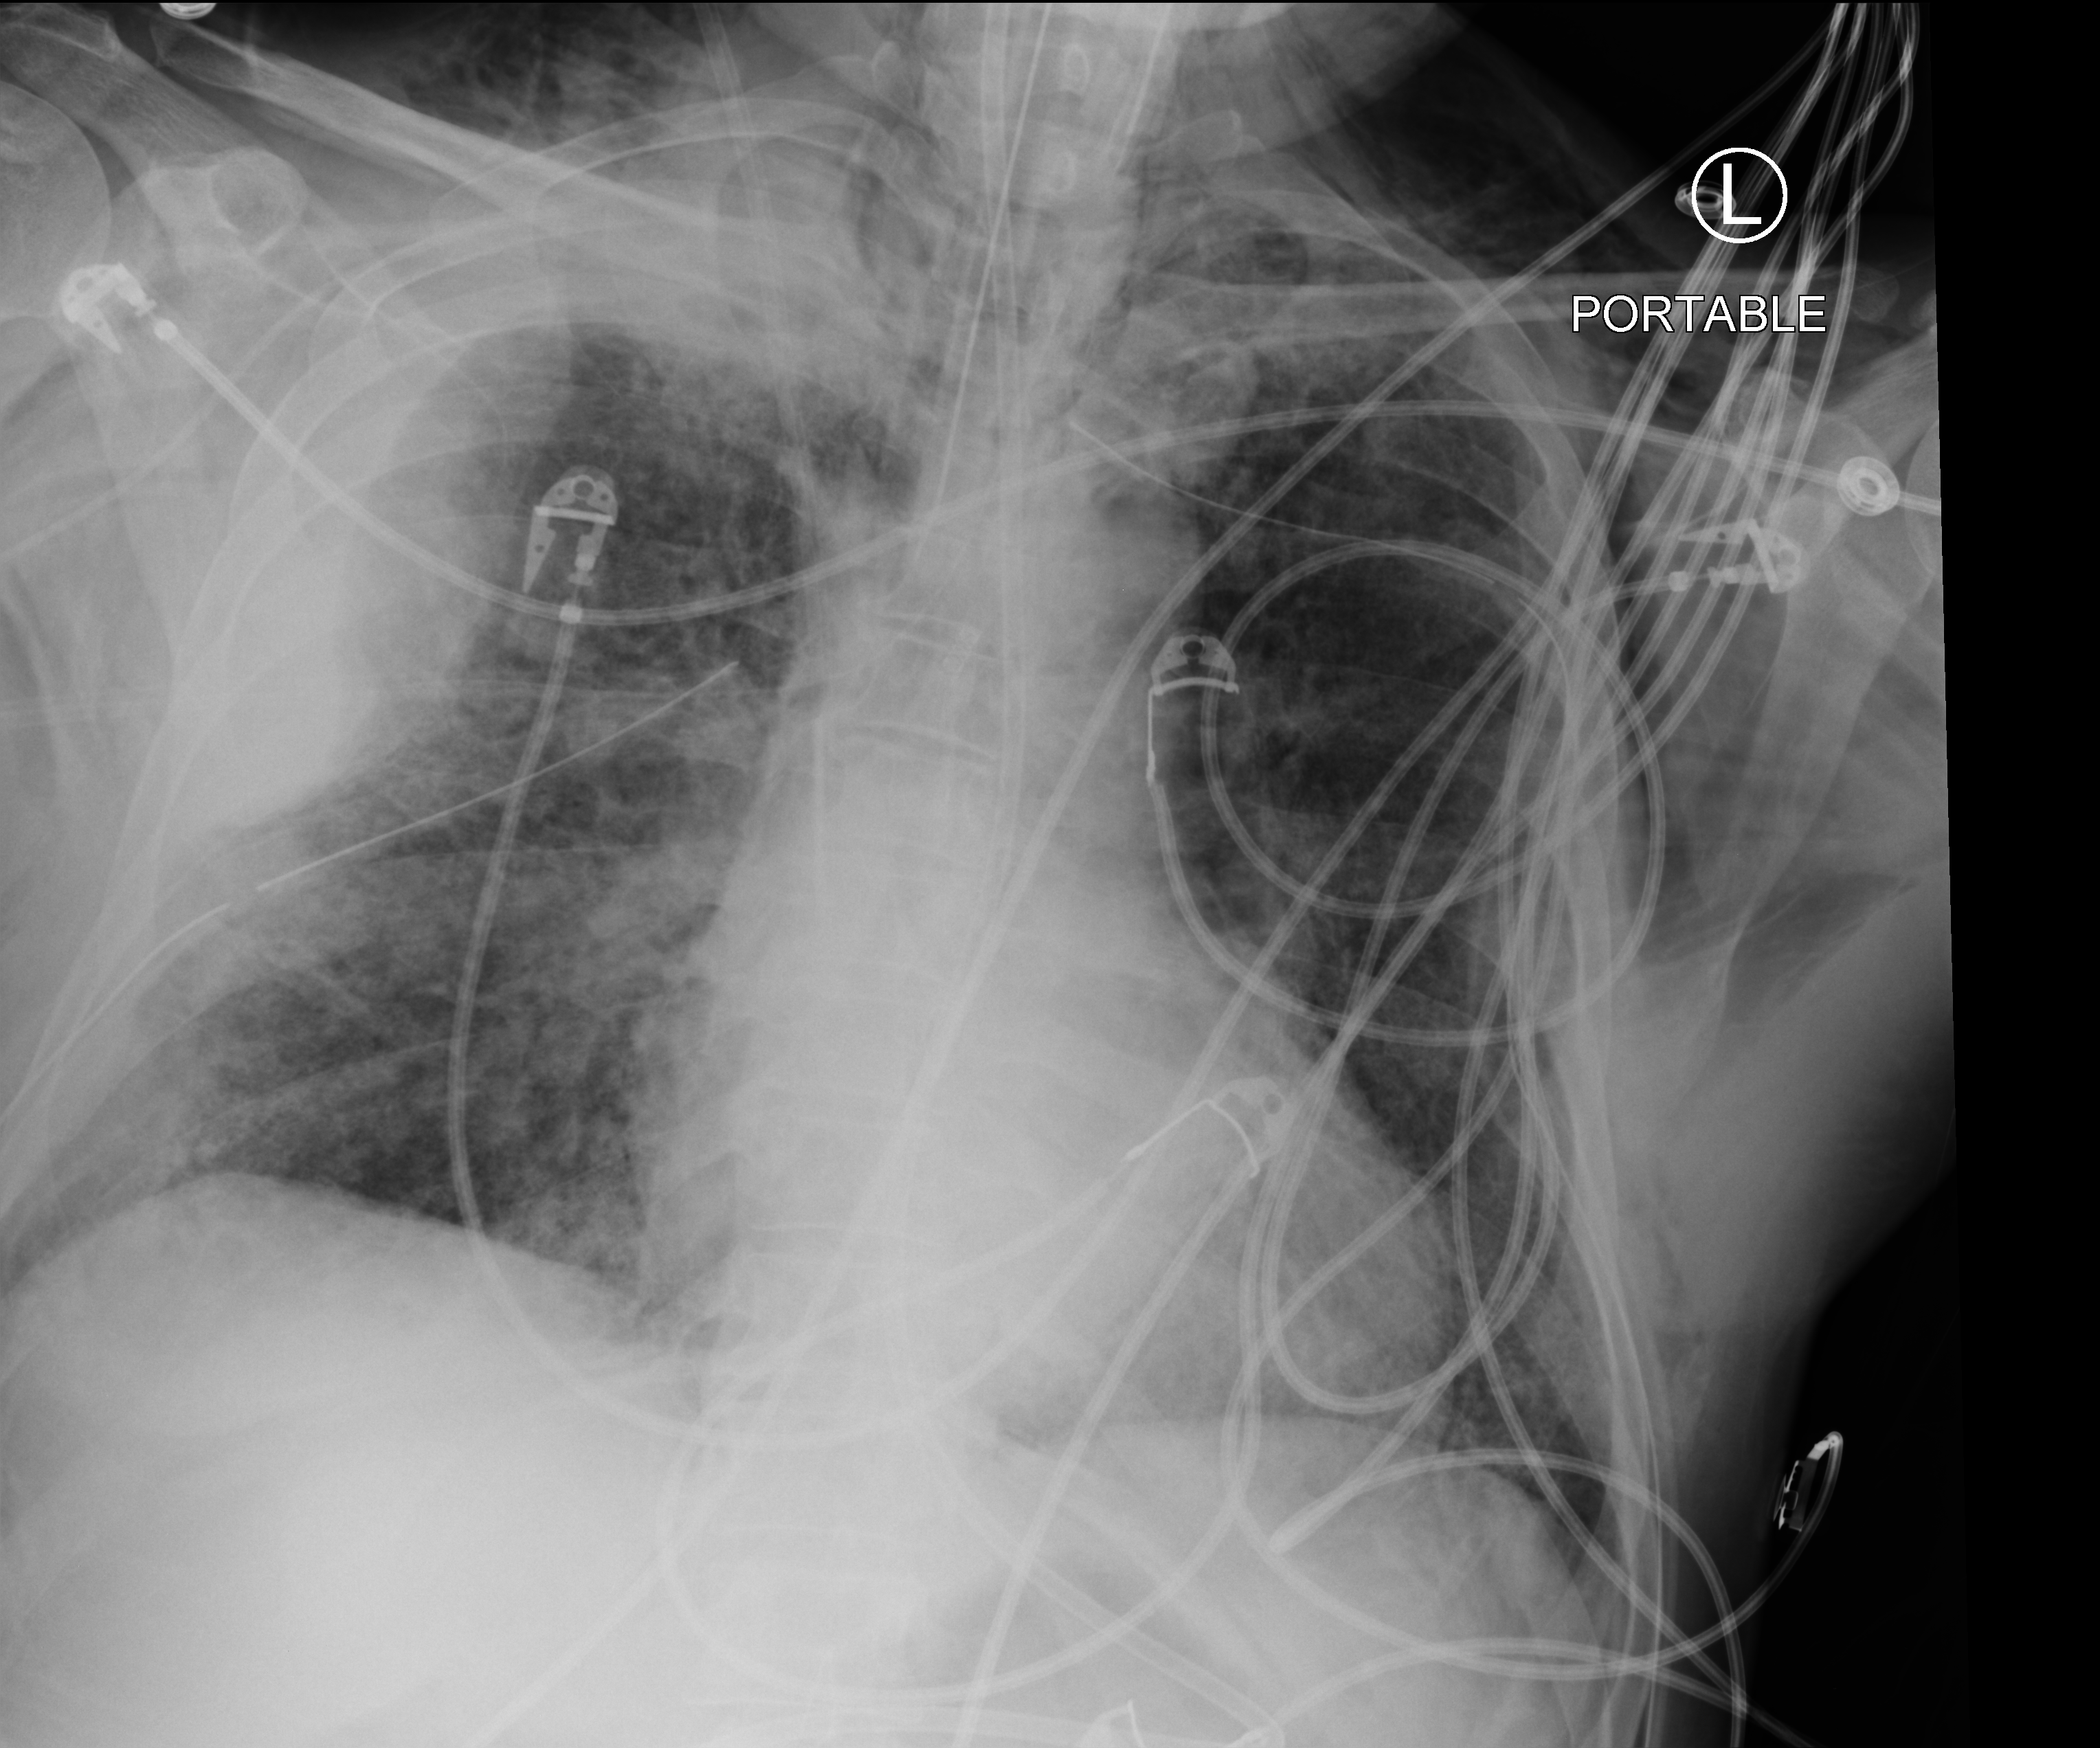
Portable chest radiograph; anteroposterior (AP) projection. Patient hospitalised with COVID-19; male, aged 18–59 years.
From the hospital-stay record, not from the radiograph (when in the stay this image was taken is not recorded):
- diabetes (admission record): no